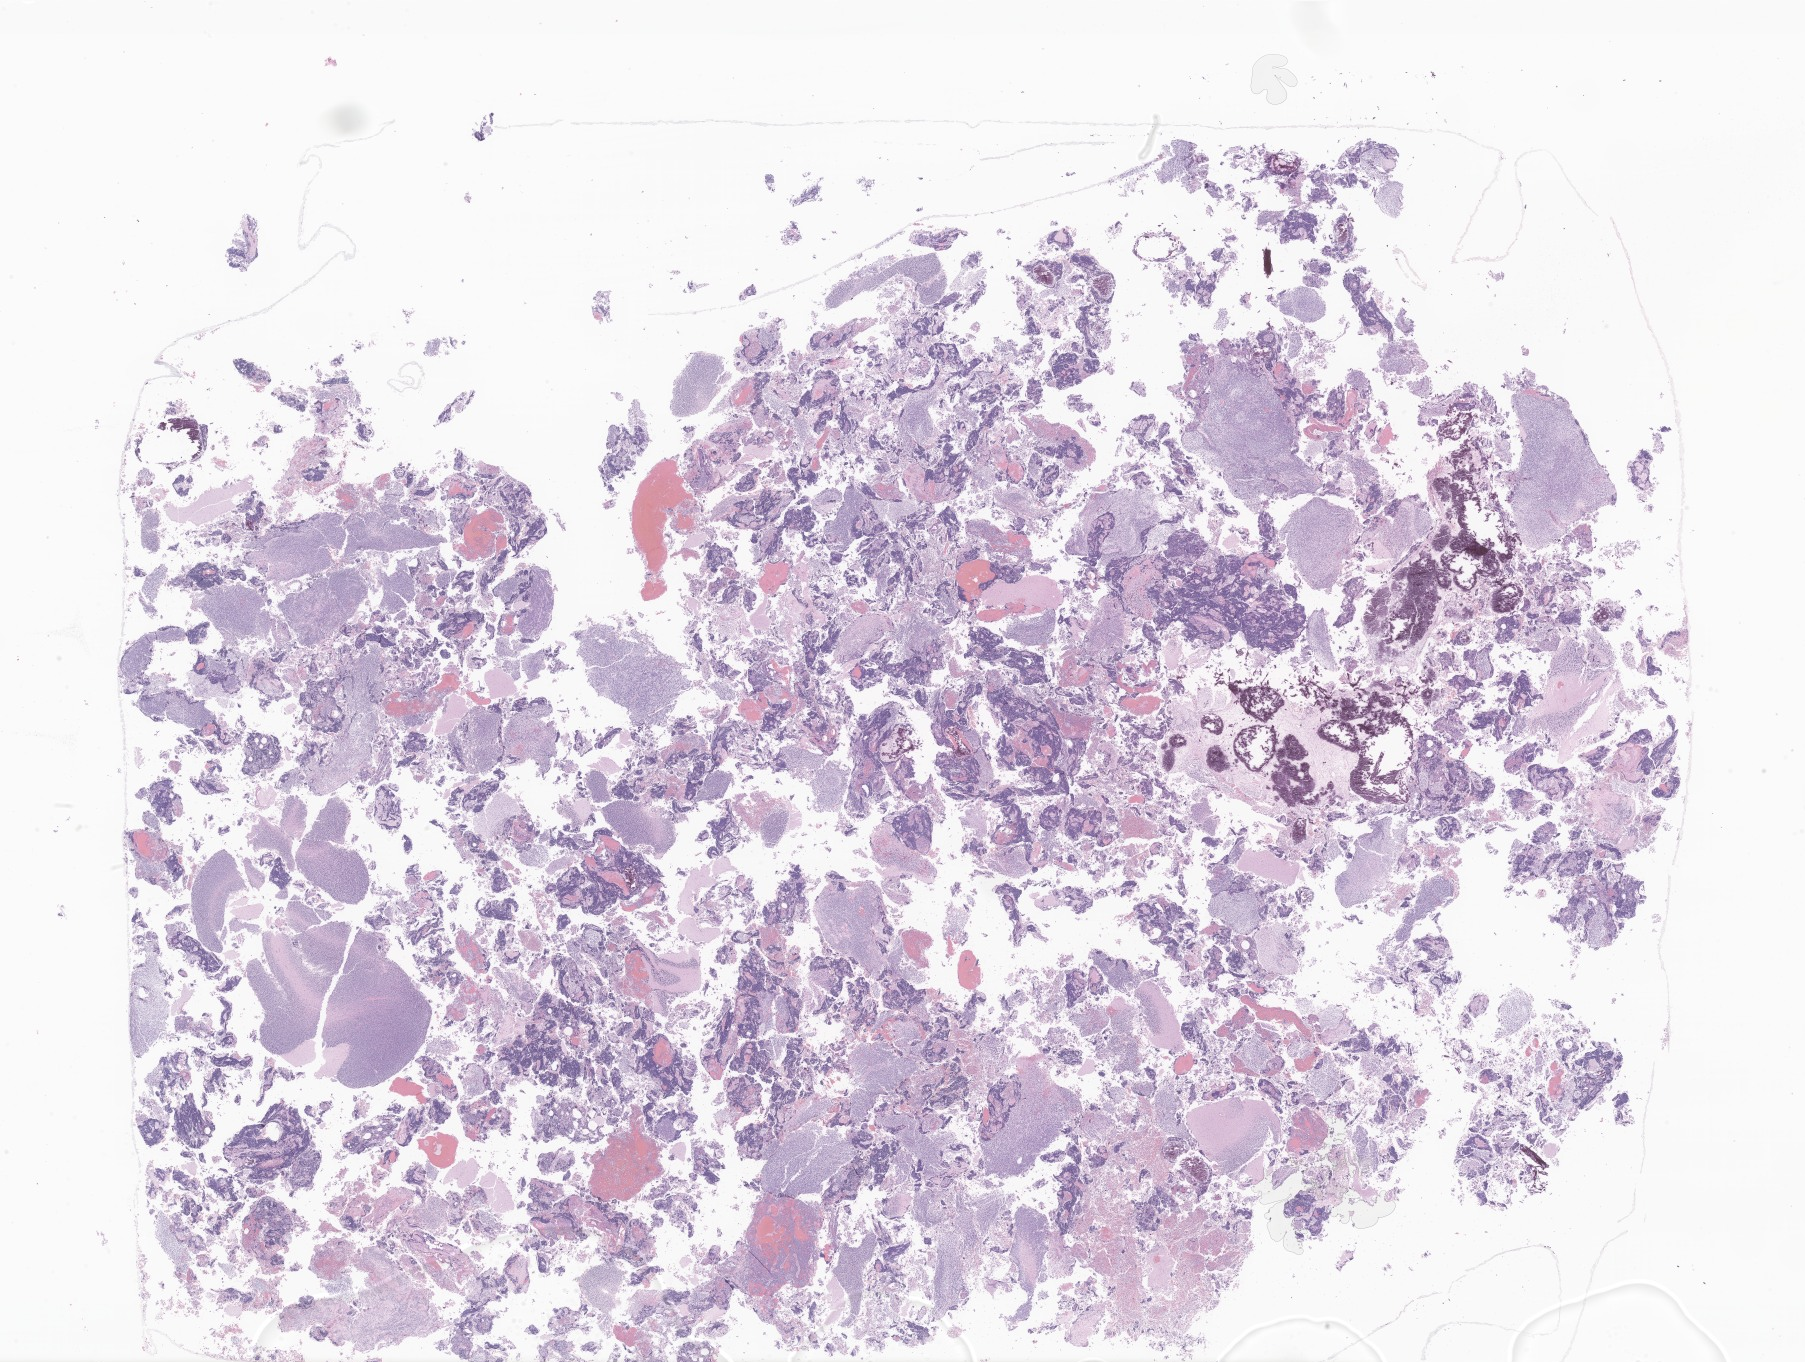
Whole-slide image, hematoxylin and eosin (H&E) stain of tumor tissue from the cerebellum — low-resolution overview of the scanned area, about 30.5 x 23.0 mm; formalin-fixed paraffin-embedded section. Male patient, age 78 months (6 years 6 months).
Recorded diagnosis: Medulloblastoma, NOS.